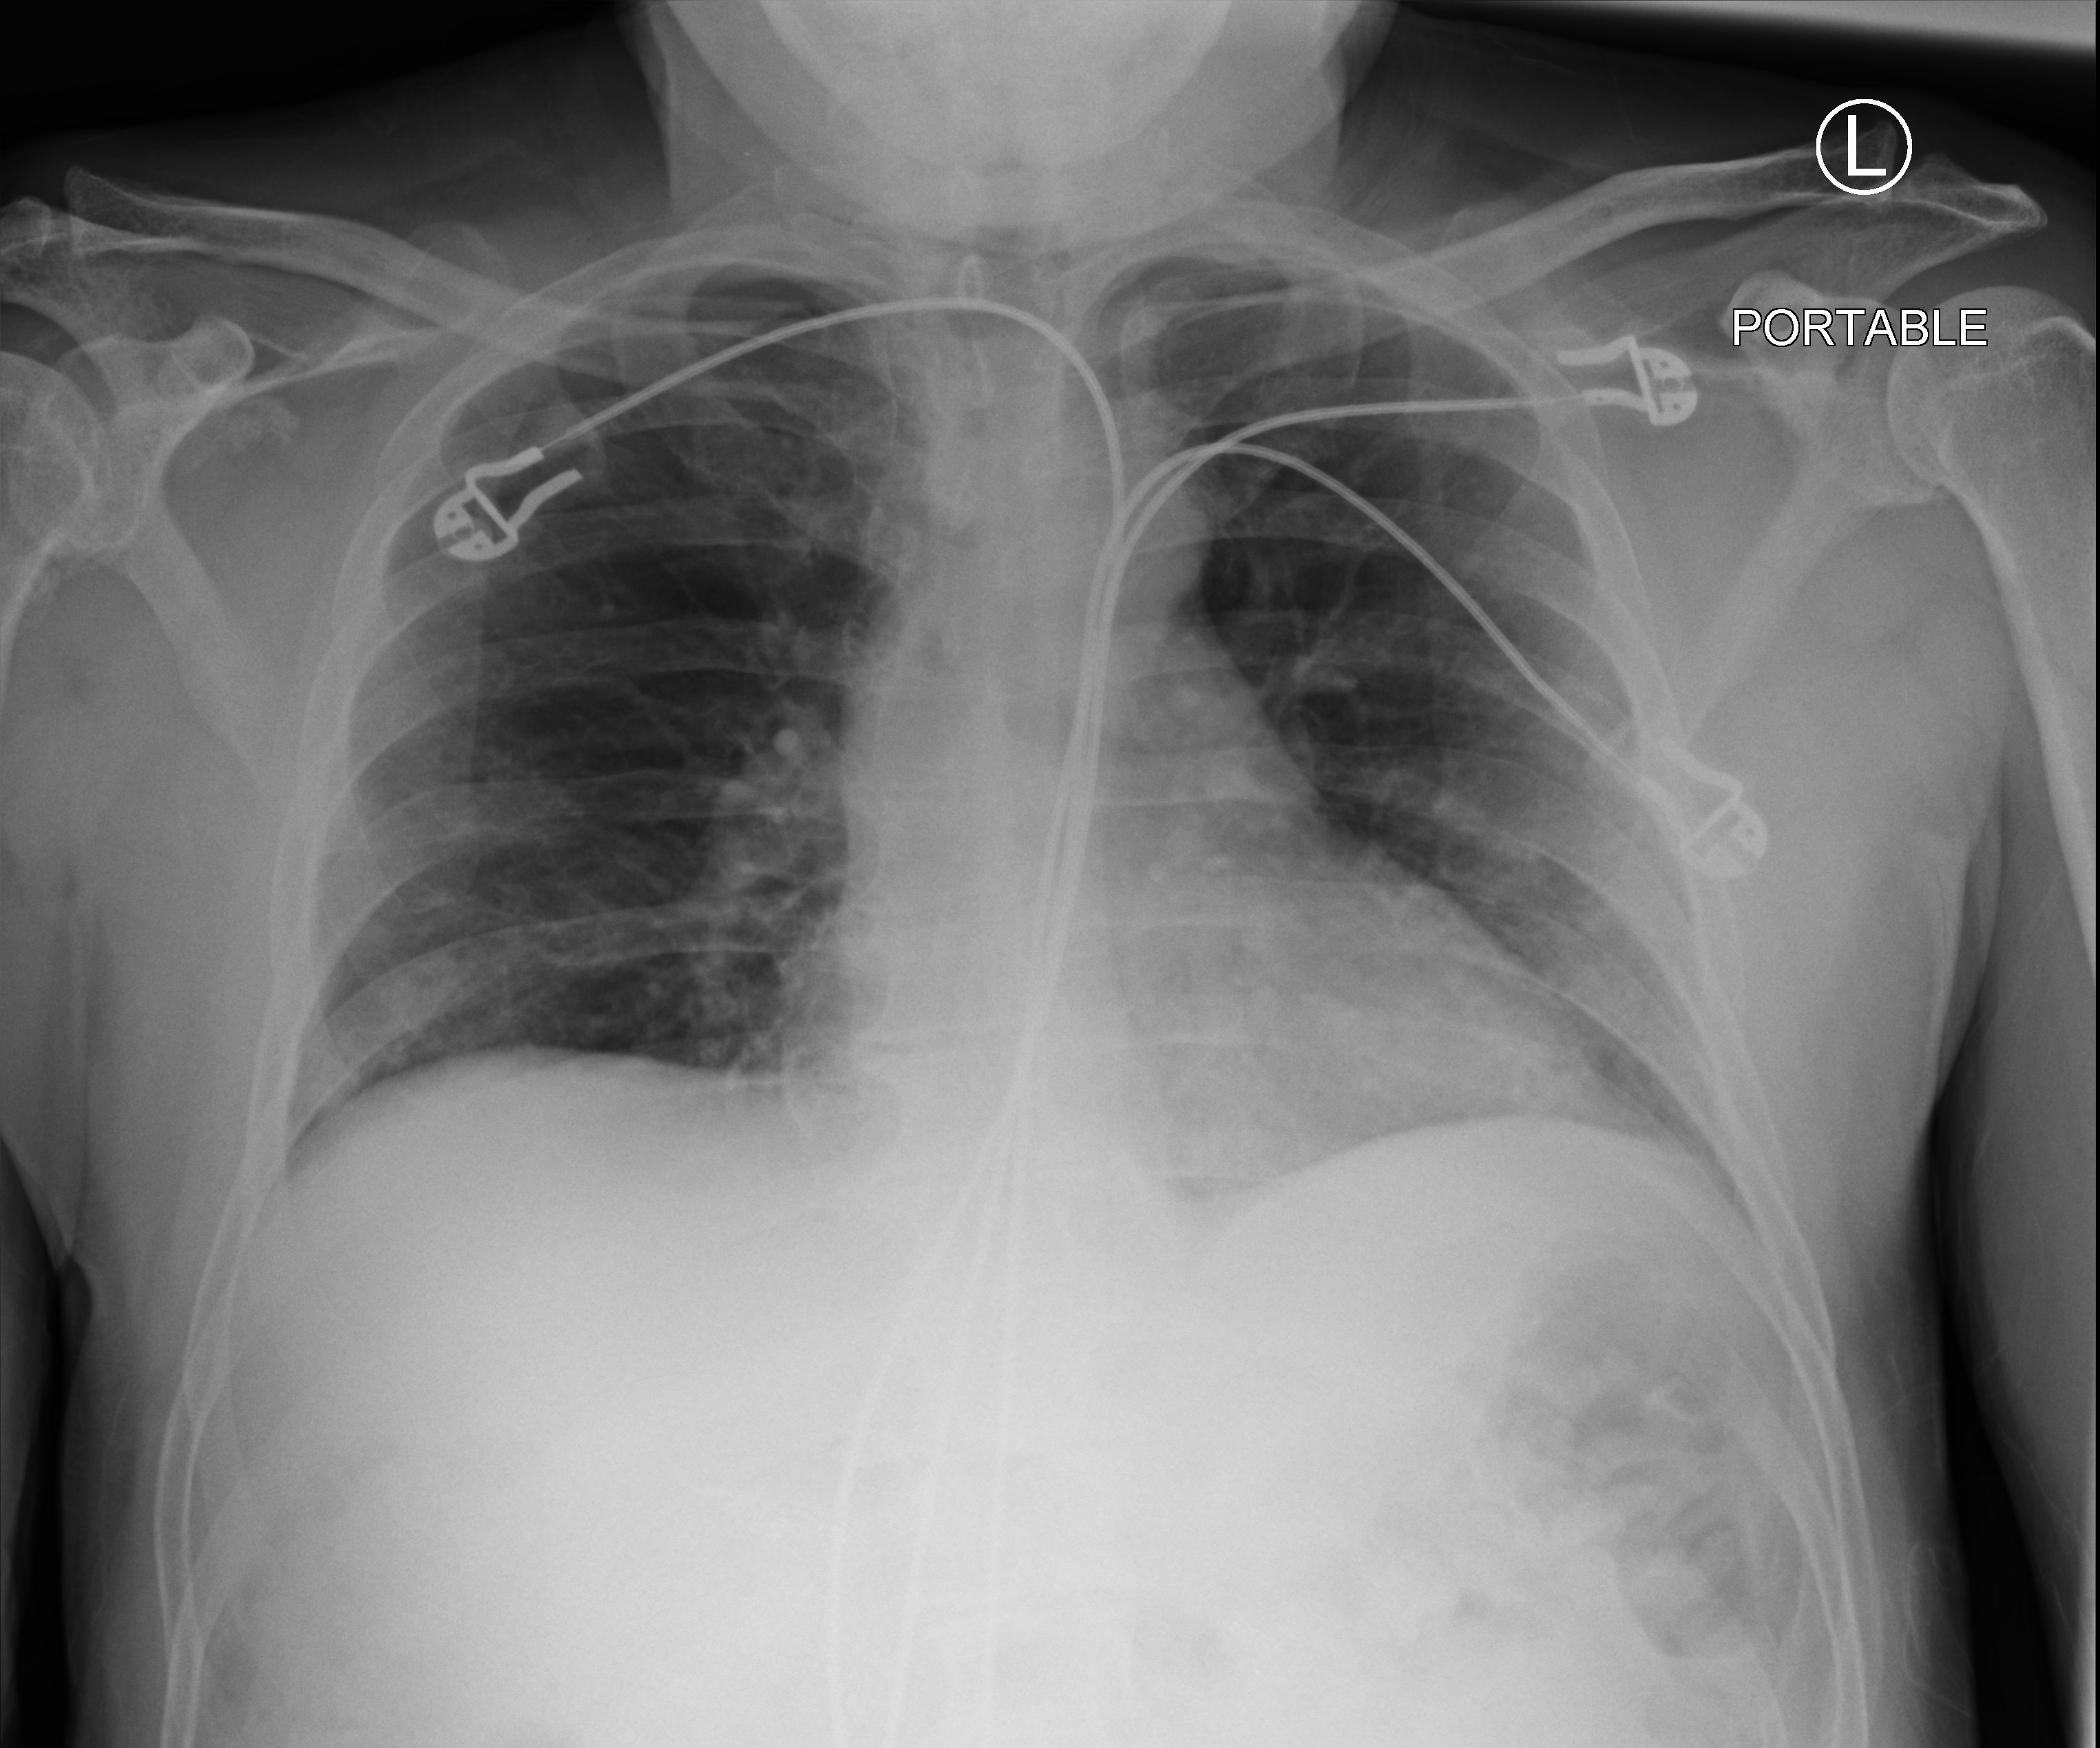
Portable chest radiograph, anteroposterior (AP) projection. Patient hospitalised with COVID-19; male, aged 18–59 years.
Hospital-stay facts (about this admission, not read from this image; timing relative to this image not recorded):
- chronic kidney disease (admission record): no